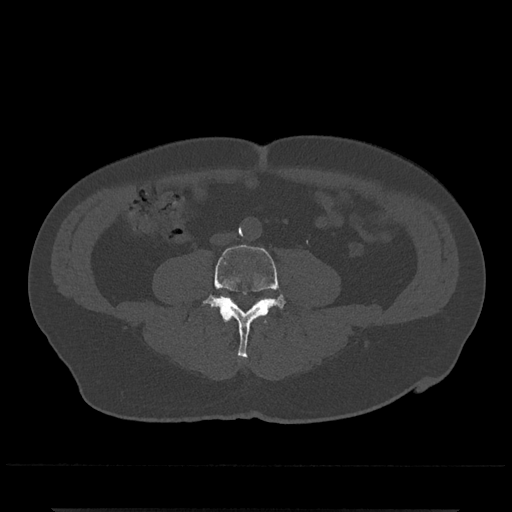
CT including the spine, one axial slice. Position 149 of 797 along the scan axis. Reconstruction kernel Br40s/3. 120 kVp. Bone window (W 1800 / L 400 HU). 0.5 mm slice thickness. 512 × 512 image matrix, field of view 393 × 393 mm. Male patient, age 67 years. From the clinical record (not read from this slice): primary cancer: prostate.
Structures marked on this image (semi-automatically segmented with operator editing):
- L3 vertebra: bounding box <223,318,266,323> (left, top, right, bottom; pixels)
- L4 vertebra: <203,244,286,358>